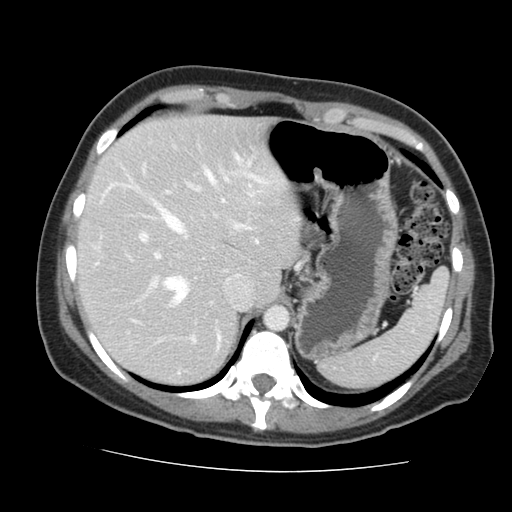
Contrast-enhanced abdominal CT, one axial slice; slice 111 of 144 in the series (ordered by position); 120 kVp; intravenous contrast given; soft-tissue window (W 400 / L 40 HU); 512 × 512 image matrix. Female patient, age 46 years. Case-level facts recorded for this patient, not image findings: diagnosis: colorectal cancer liver metastases, imaged before liver resection; multiple liver metastases: no; largest metastasis: 2.8 cm; disease in both lobes: no.
Annotated regions visible in this slice (outlined manually by an expert reader):
- hepatic veins: bounding box (x1, y1, x2, y2) in pixels: (103, 167, 214, 304)
- liver: (80, 117, 296, 383)
- planned liver remnant (the part of the liver to remain after resection): (80, 117, 296, 383)
- portal vein (with intrahepatic branches): (140, 174, 251, 342)